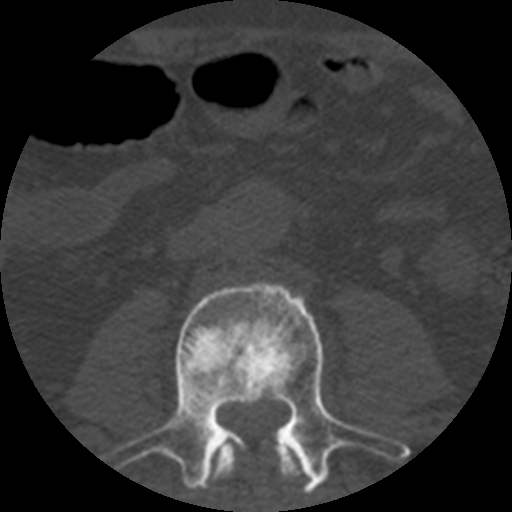
CT including the spine, one axial slice. Position 126 of 508 along the scan axis. 120 kVp. Bone window (W 1800 / L 400 HU). 1.25 mm slice thickness. 512 × 512 image matrix, field of view 160 × 160 mm. Patient age 57 years. From the clinical record (not read from this slice): primary cancer: prostate.
Annotated regions visible in this slice (semi-automatically segmented with operator editing):
- L2 vertebra: box from (x=210, y=436) to (x=309, y=494) px
- L3 vertebra: (x=97, y=283)–(x=410, y=493)